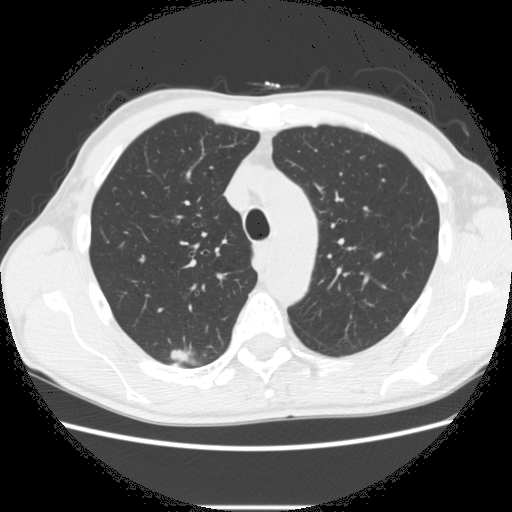
Low-dose screening chest CT, axial slice. Second screening round (one year after baseline). Lung window (W 1500 / L -600 HU). 2.5 mm slice thickness. Standard (soft-tissue) reconstruction kernel (STANDARD). 120 kVp. Slice 74 of 282 in the series. Male participant, aged 66 years at enrolment. Former smoker at enrolment.
• Lesion marked by an expert reader, bounding box (x1, y1, x2, y2) in pixels: (160, 336, 222, 372).
• The screening reader recorded 5 non-calcified nodules or masses ≥4 mm on this exam; which of them this box marks is not recorded.
• Later outcome: lung cancer diagnosed 75 days after this screen — adenocarcinoma, NOS, right upper lobe, undifferentiated (G4), stage IA (AJCC 6th edition), 20 mm at pathology.